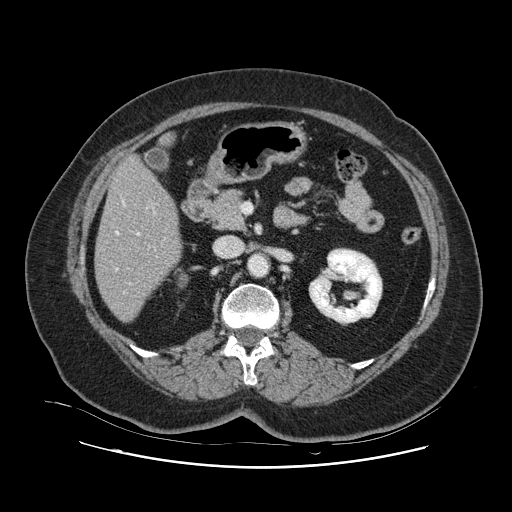
Contrast-enhanced abdominal CT, one axial slice. Position 42 of 132 along the scan axis. 120 kVp. Intravenous contrast given. Soft-tissue window (W 400 / L 40 HU). 2.5 mm slice thickness. 512 × 512 image matrix. Female patient, age 73 years. Case-level facts recorded for this patient, not image findings: diagnosis: colorectal cancer liver metastases, imaged before liver resection; multiple liver metastases: no; largest metastasis: 7 cm; chemotherapy before resection: yes.
Outlined on this slice (outlined manually by an expert reader):
- hepatic veins: bounding box [x1, y1, x2, y2] px = [116, 201, 155, 293]
- liver: [96, 158, 181, 321]
- planned liver remnant (the part of the liver to remain after resection): [96, 158, 181, 321]
- portal vein (with intrahepatic branches): [129, 233, 140, 285]